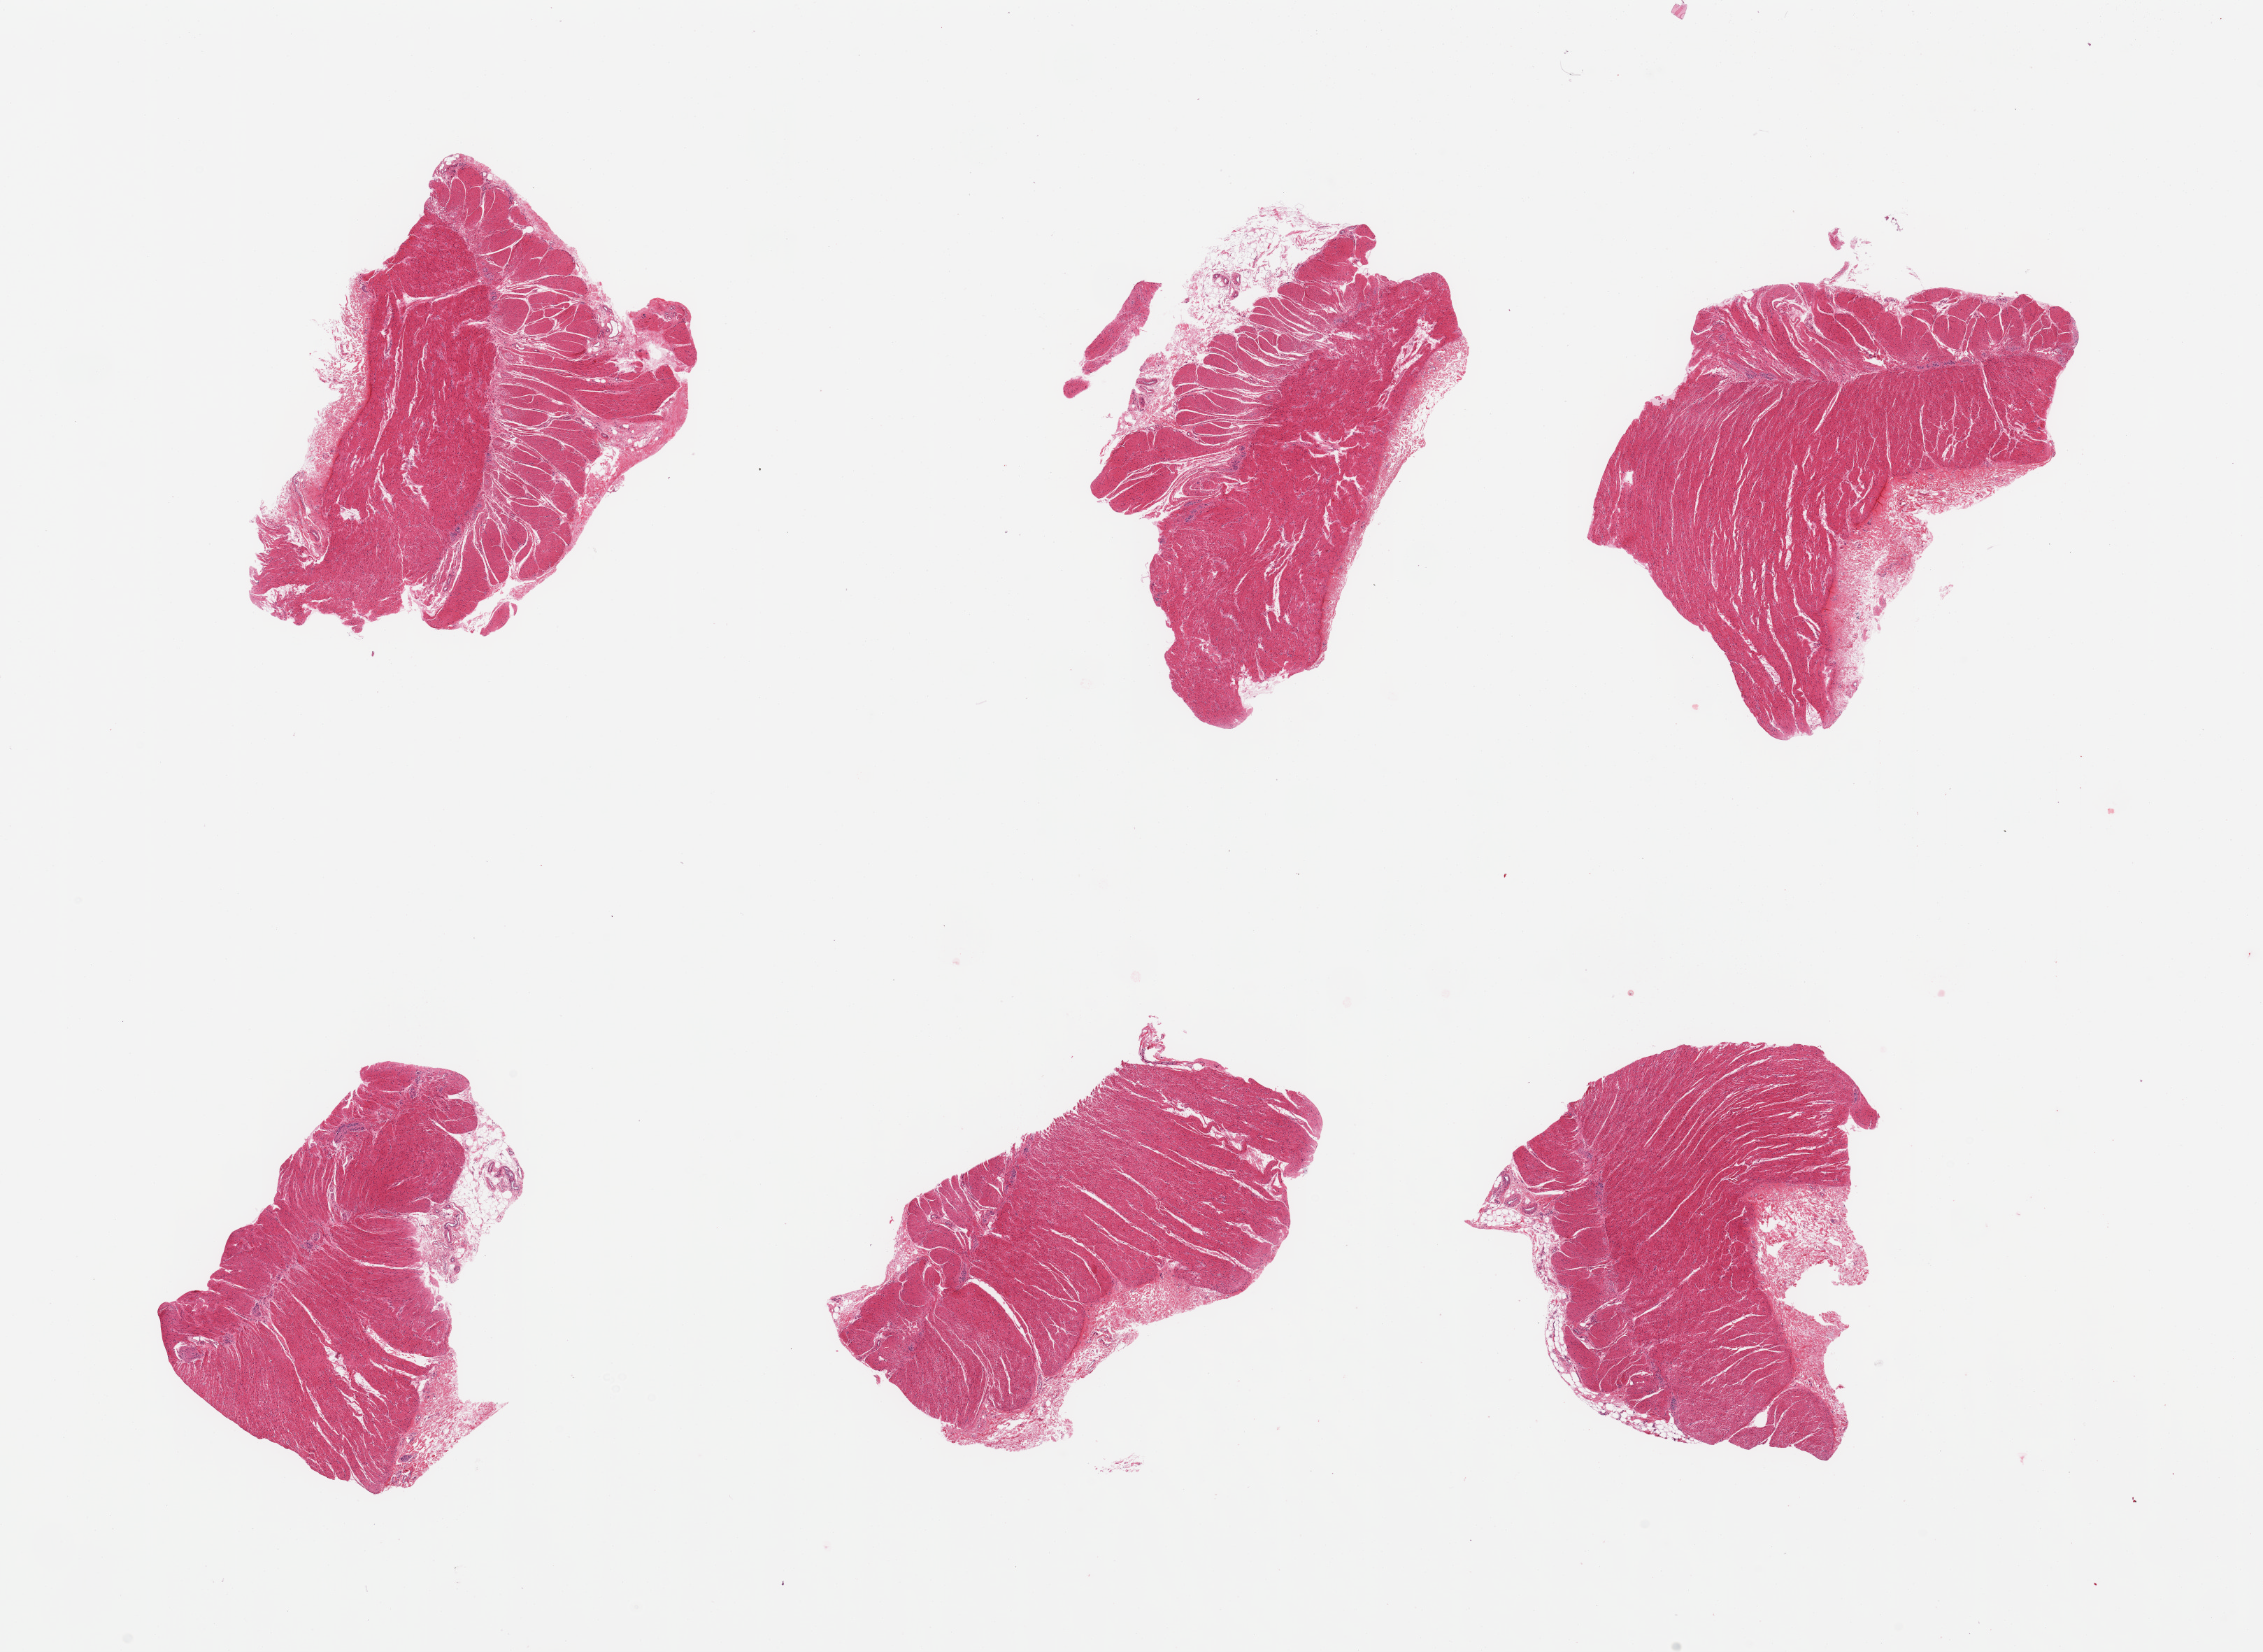
Whole-slide image, haematoxylin and eosin stain, low-resolution overview of the scanned area, about 25.6 x 18.7 mm (from a 20x scan); PAXgene-fixed, paraffin-embedded tissue; sampled site (target tissue): sigmoid colon; donor tissue sample. Donor: male.
- reviewer comment on this tissue sample: 6 pieces; target muscularis